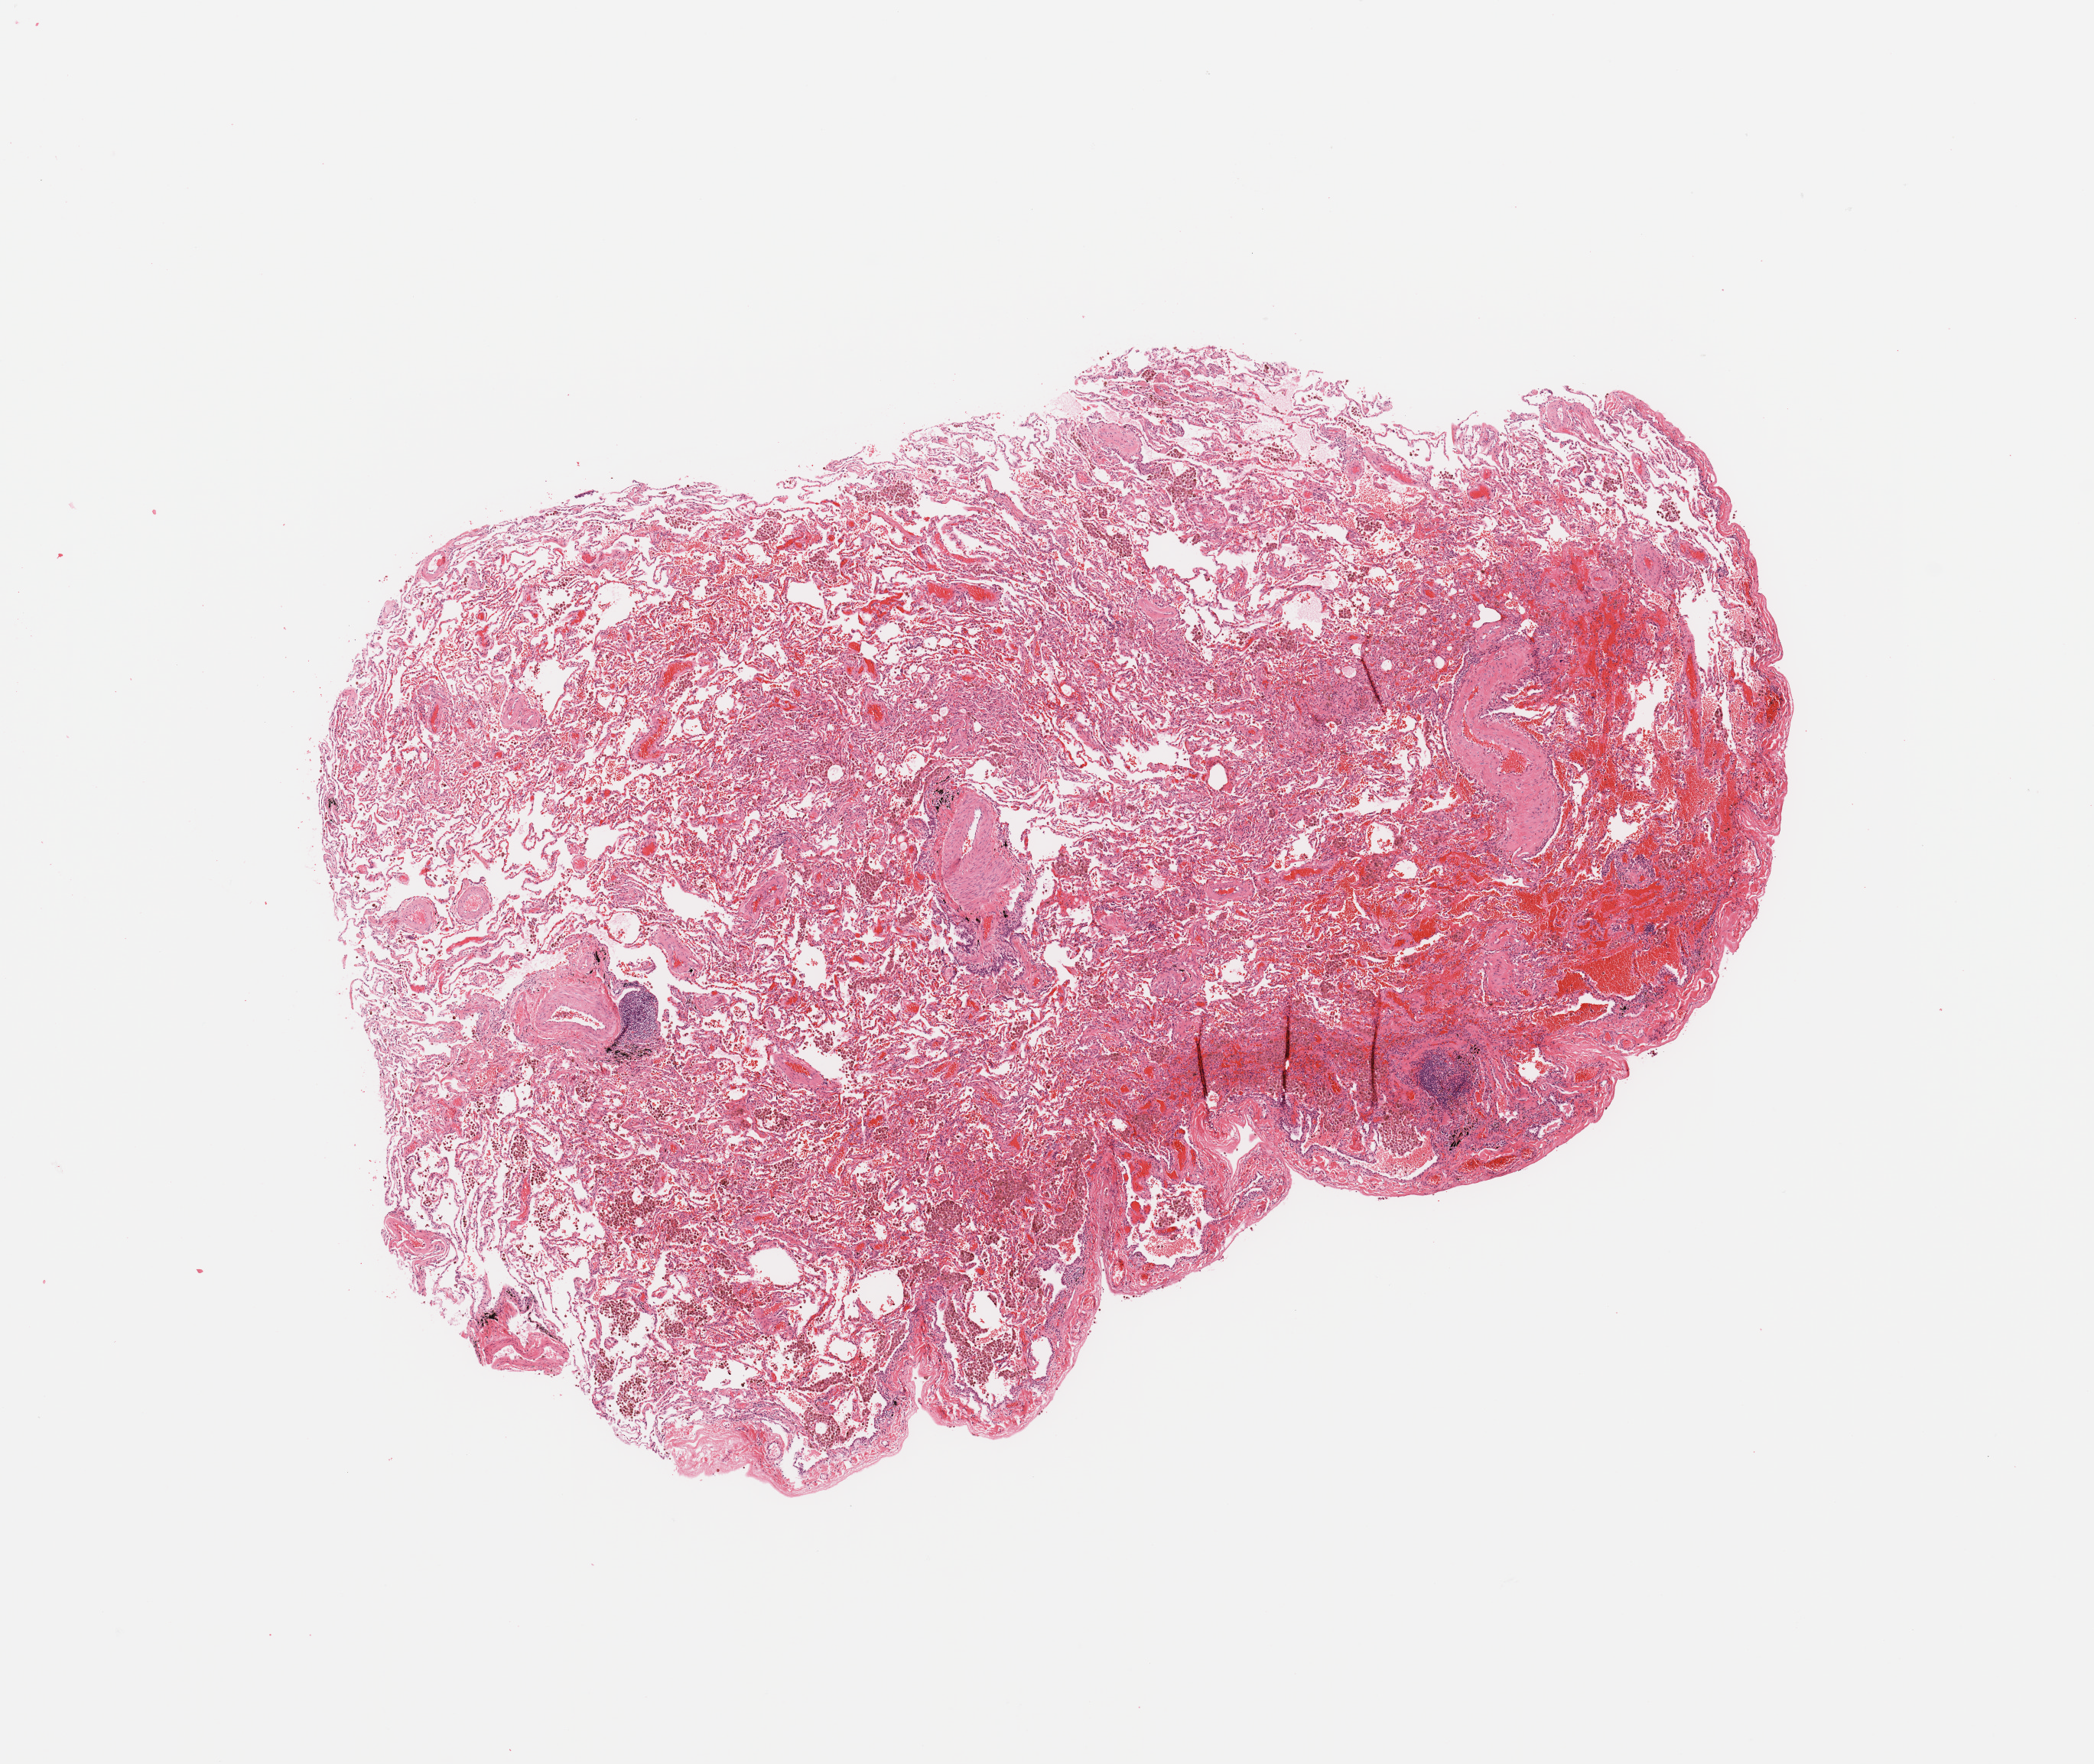
H&E whole-slide image, a low-resolution overview of the entire scanned area, about 10.8 x 9.1 mm (slide scanned at 20x); lung, normal (non-tumour) tissue. 59-year-old female patient.
This section: normal (non-tumour) tissue from the same patient. Patient diagnosis: Adenocarcinoma, NOS.